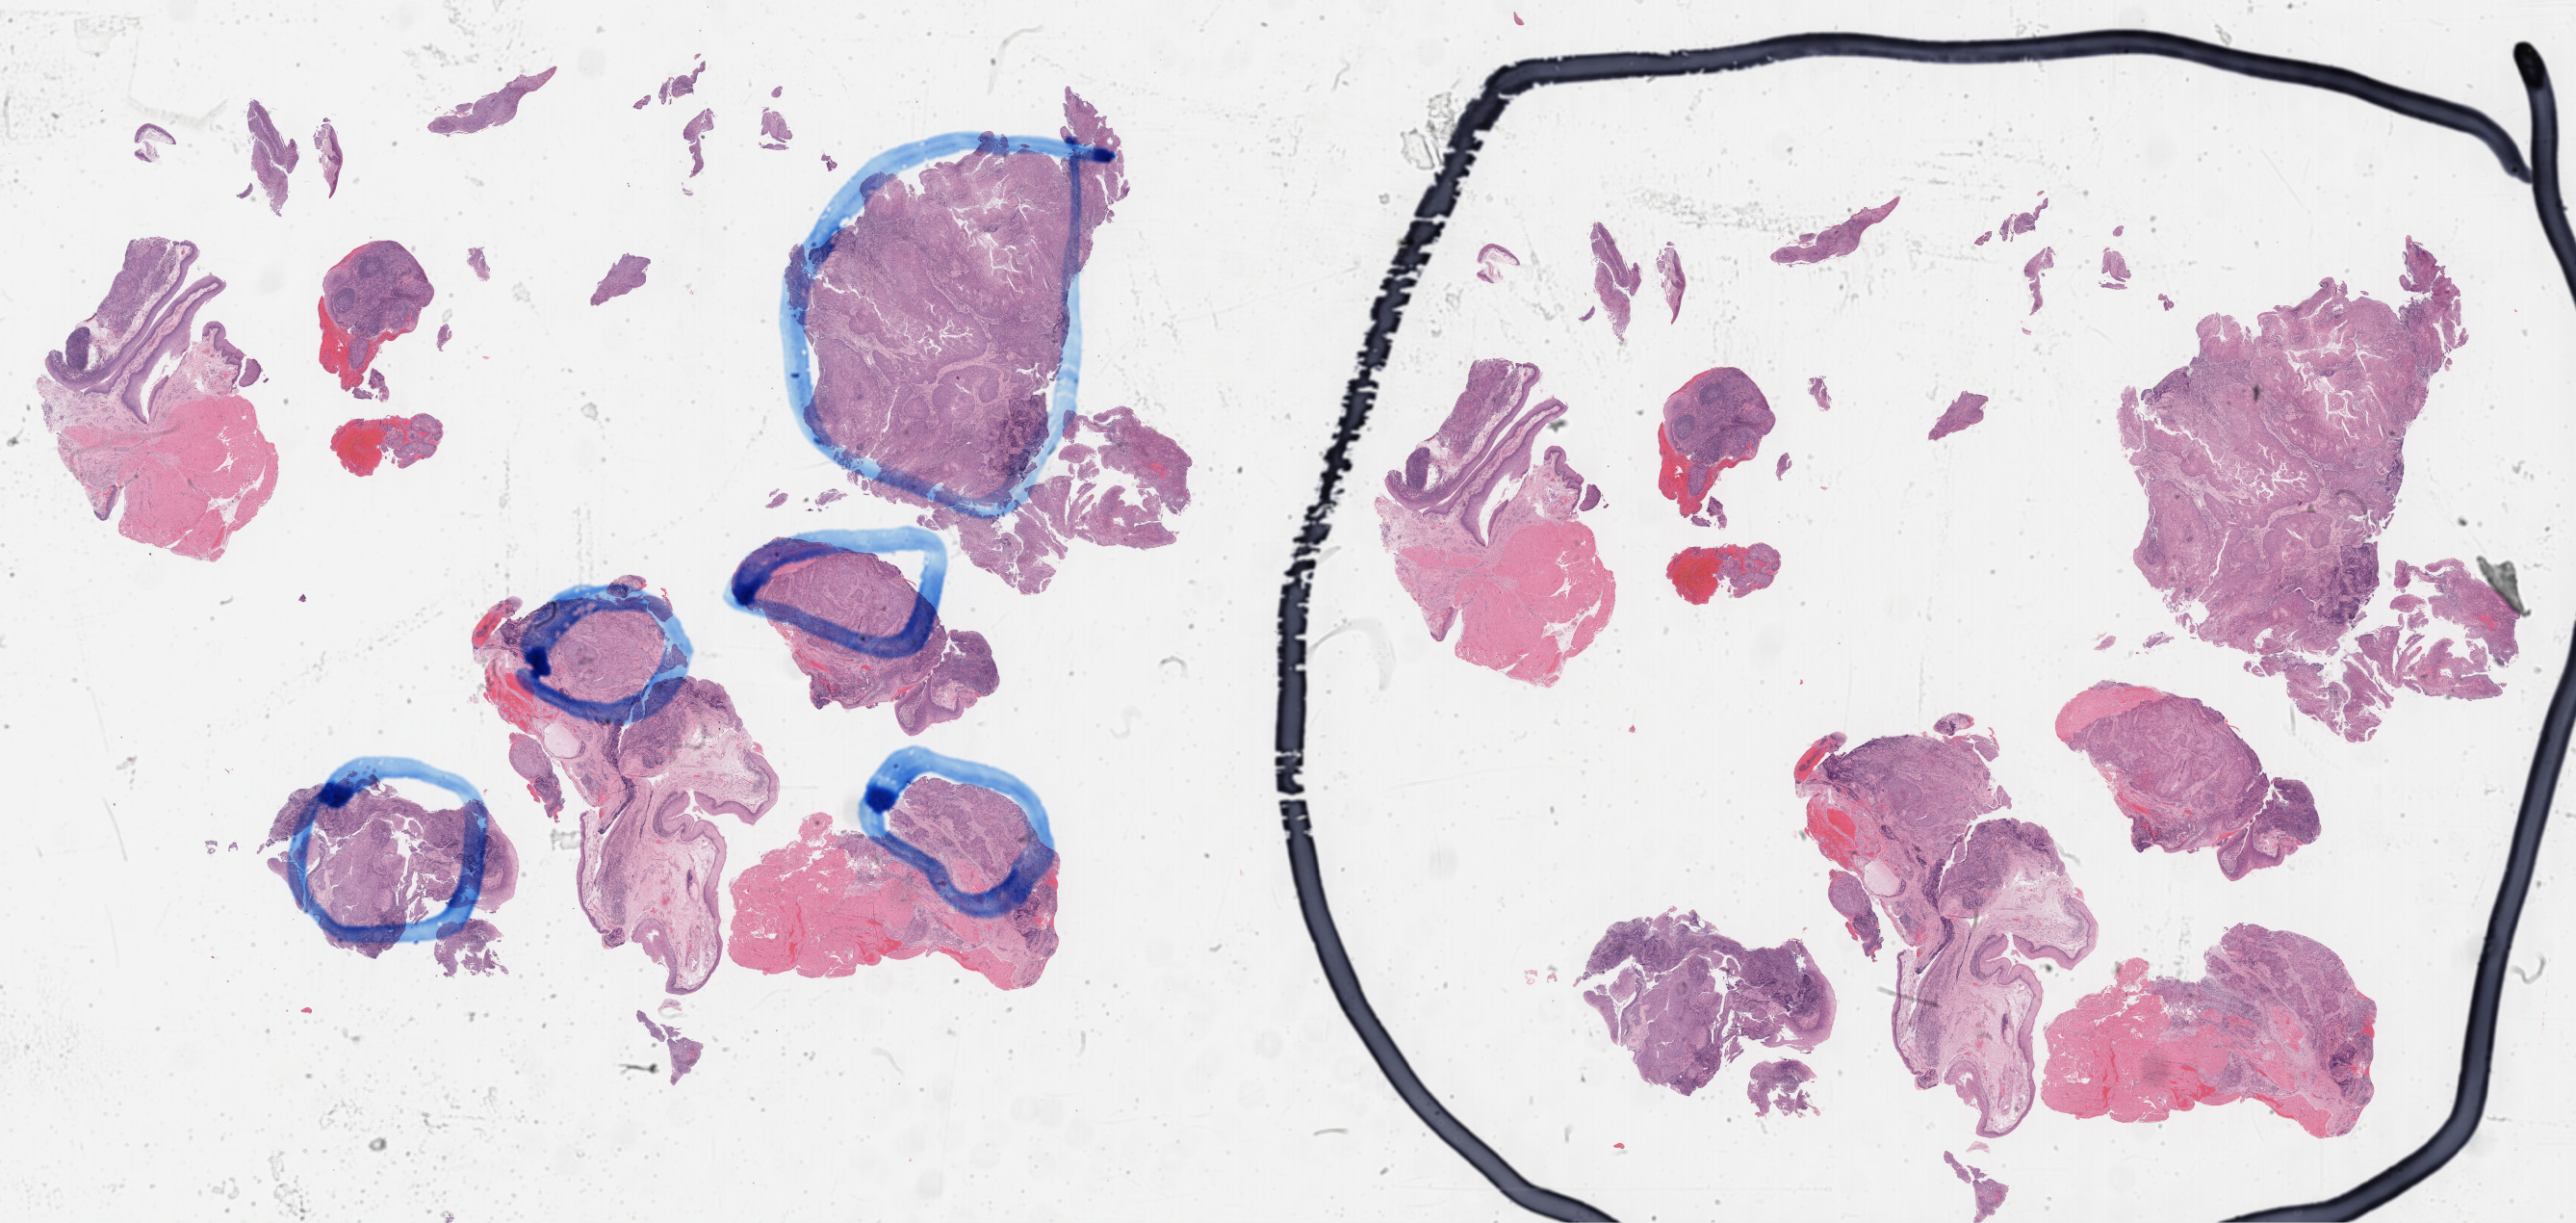
H&E whole-slide image — low-resolution overview of the scanned area, about 43.3 x 20.5 mm (from a 40x scan). FFPE section. Head and neck, primary tumour sample. Male, age 48 years at initial diagnosis. Histologic grade: G4 (undifferentiated).
Diagnosis: Squamous cell carcinoma, NOS (tonsil, NOS).